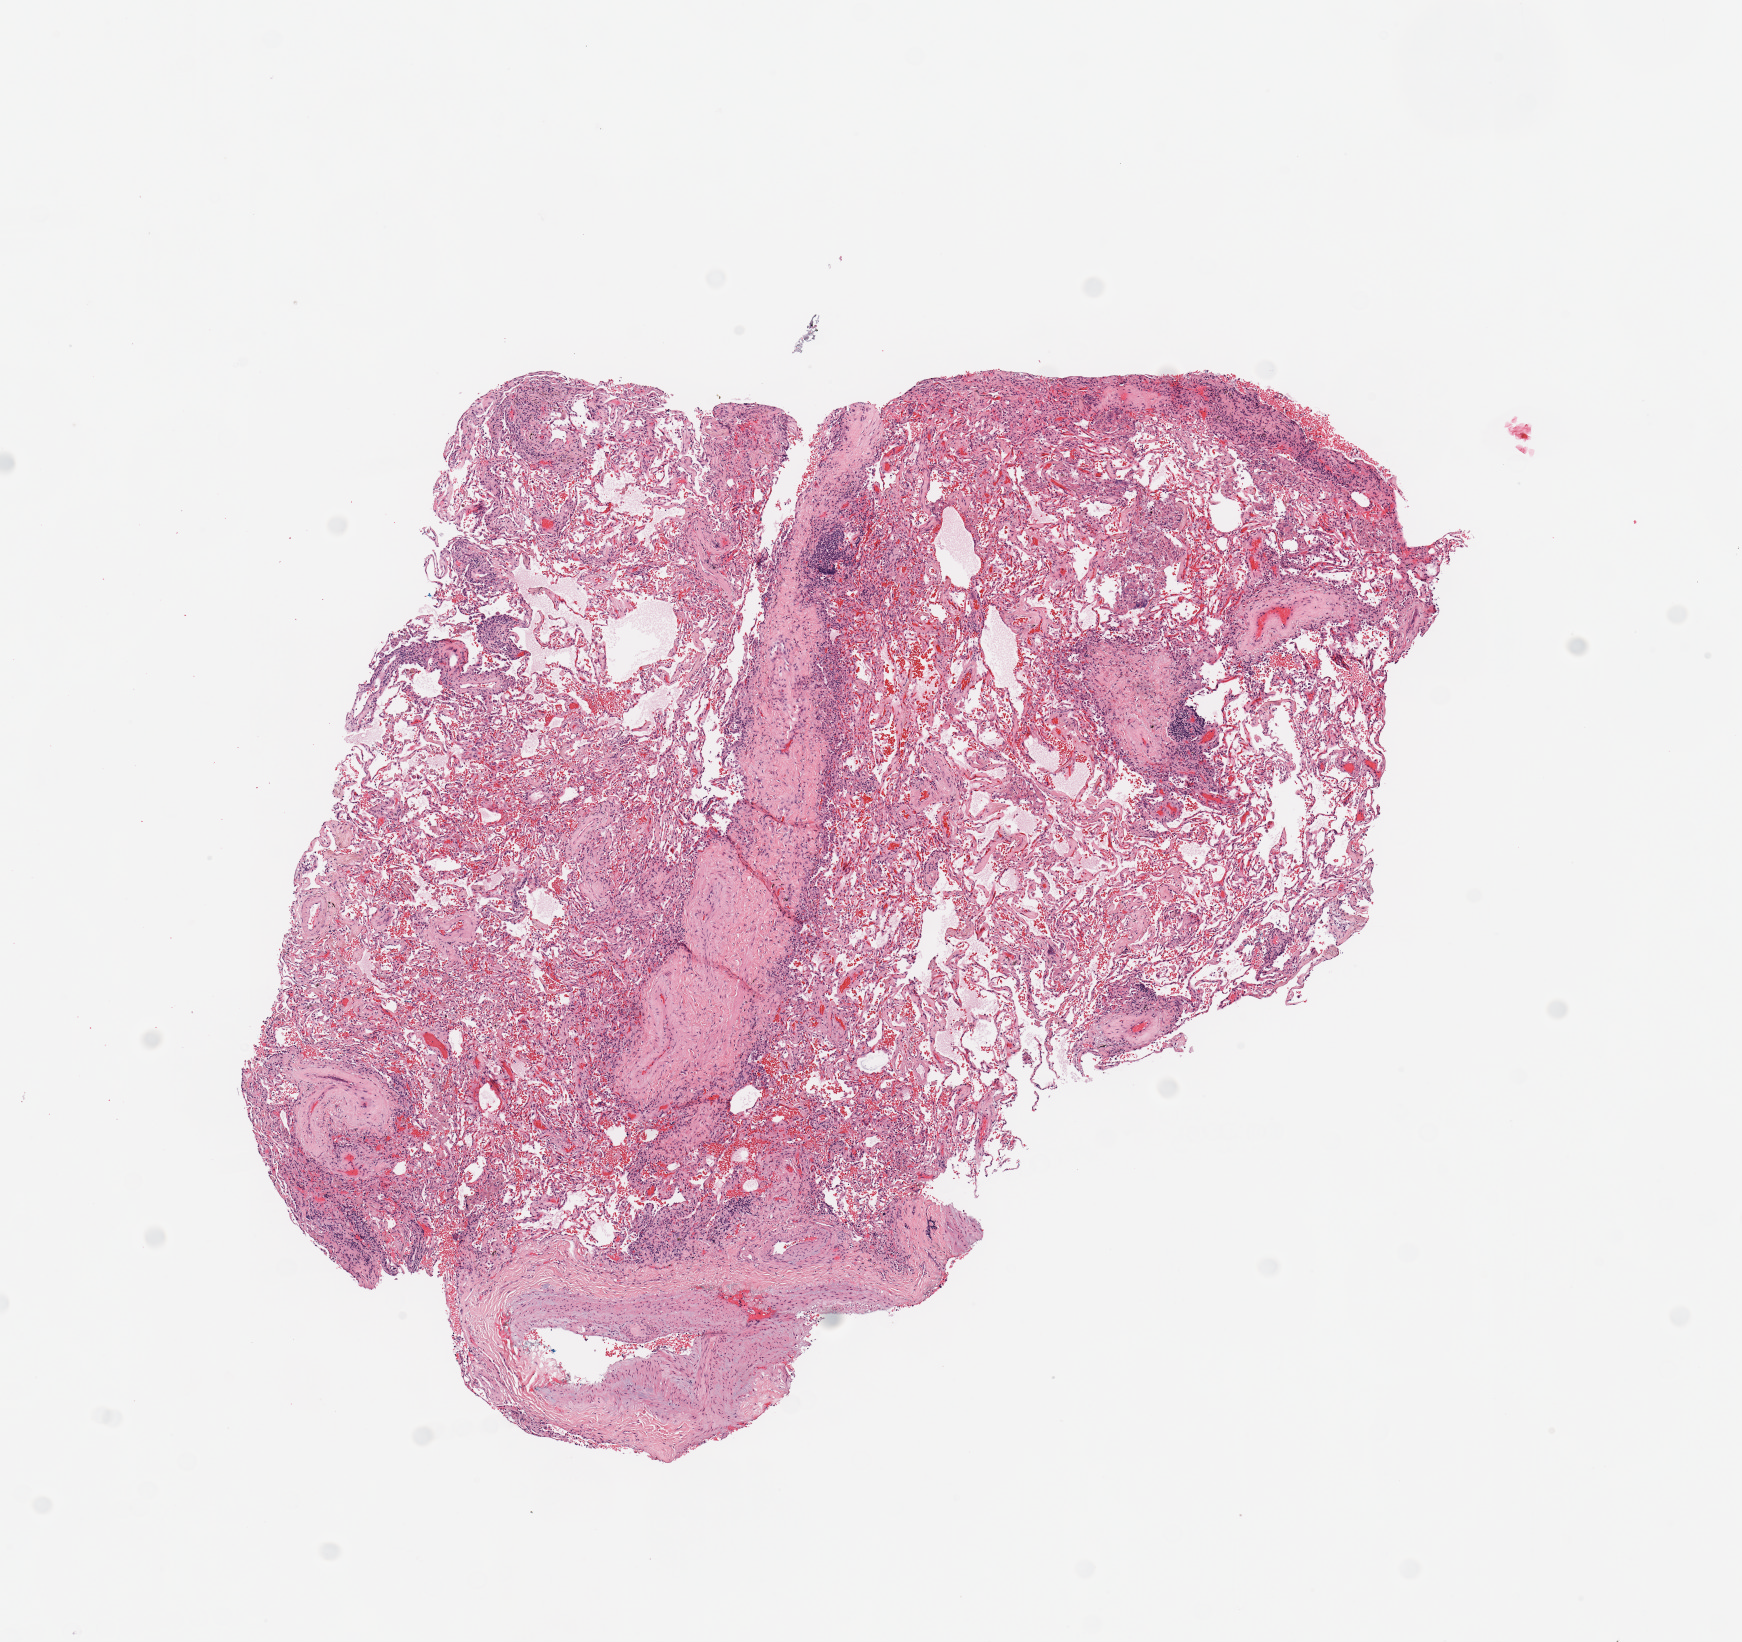
Whole-slide histology image, H&E — low-resolution overview of the scanned area, about 6.9 x 6.5 mm. Normal (non-tumour) tissue sample, sampled site: lung. Male, 69 y/o.
This section: normal (non-tumour) tissue from the same patient. Patient diagnosis: Squamous cell carcinoma, NOS.